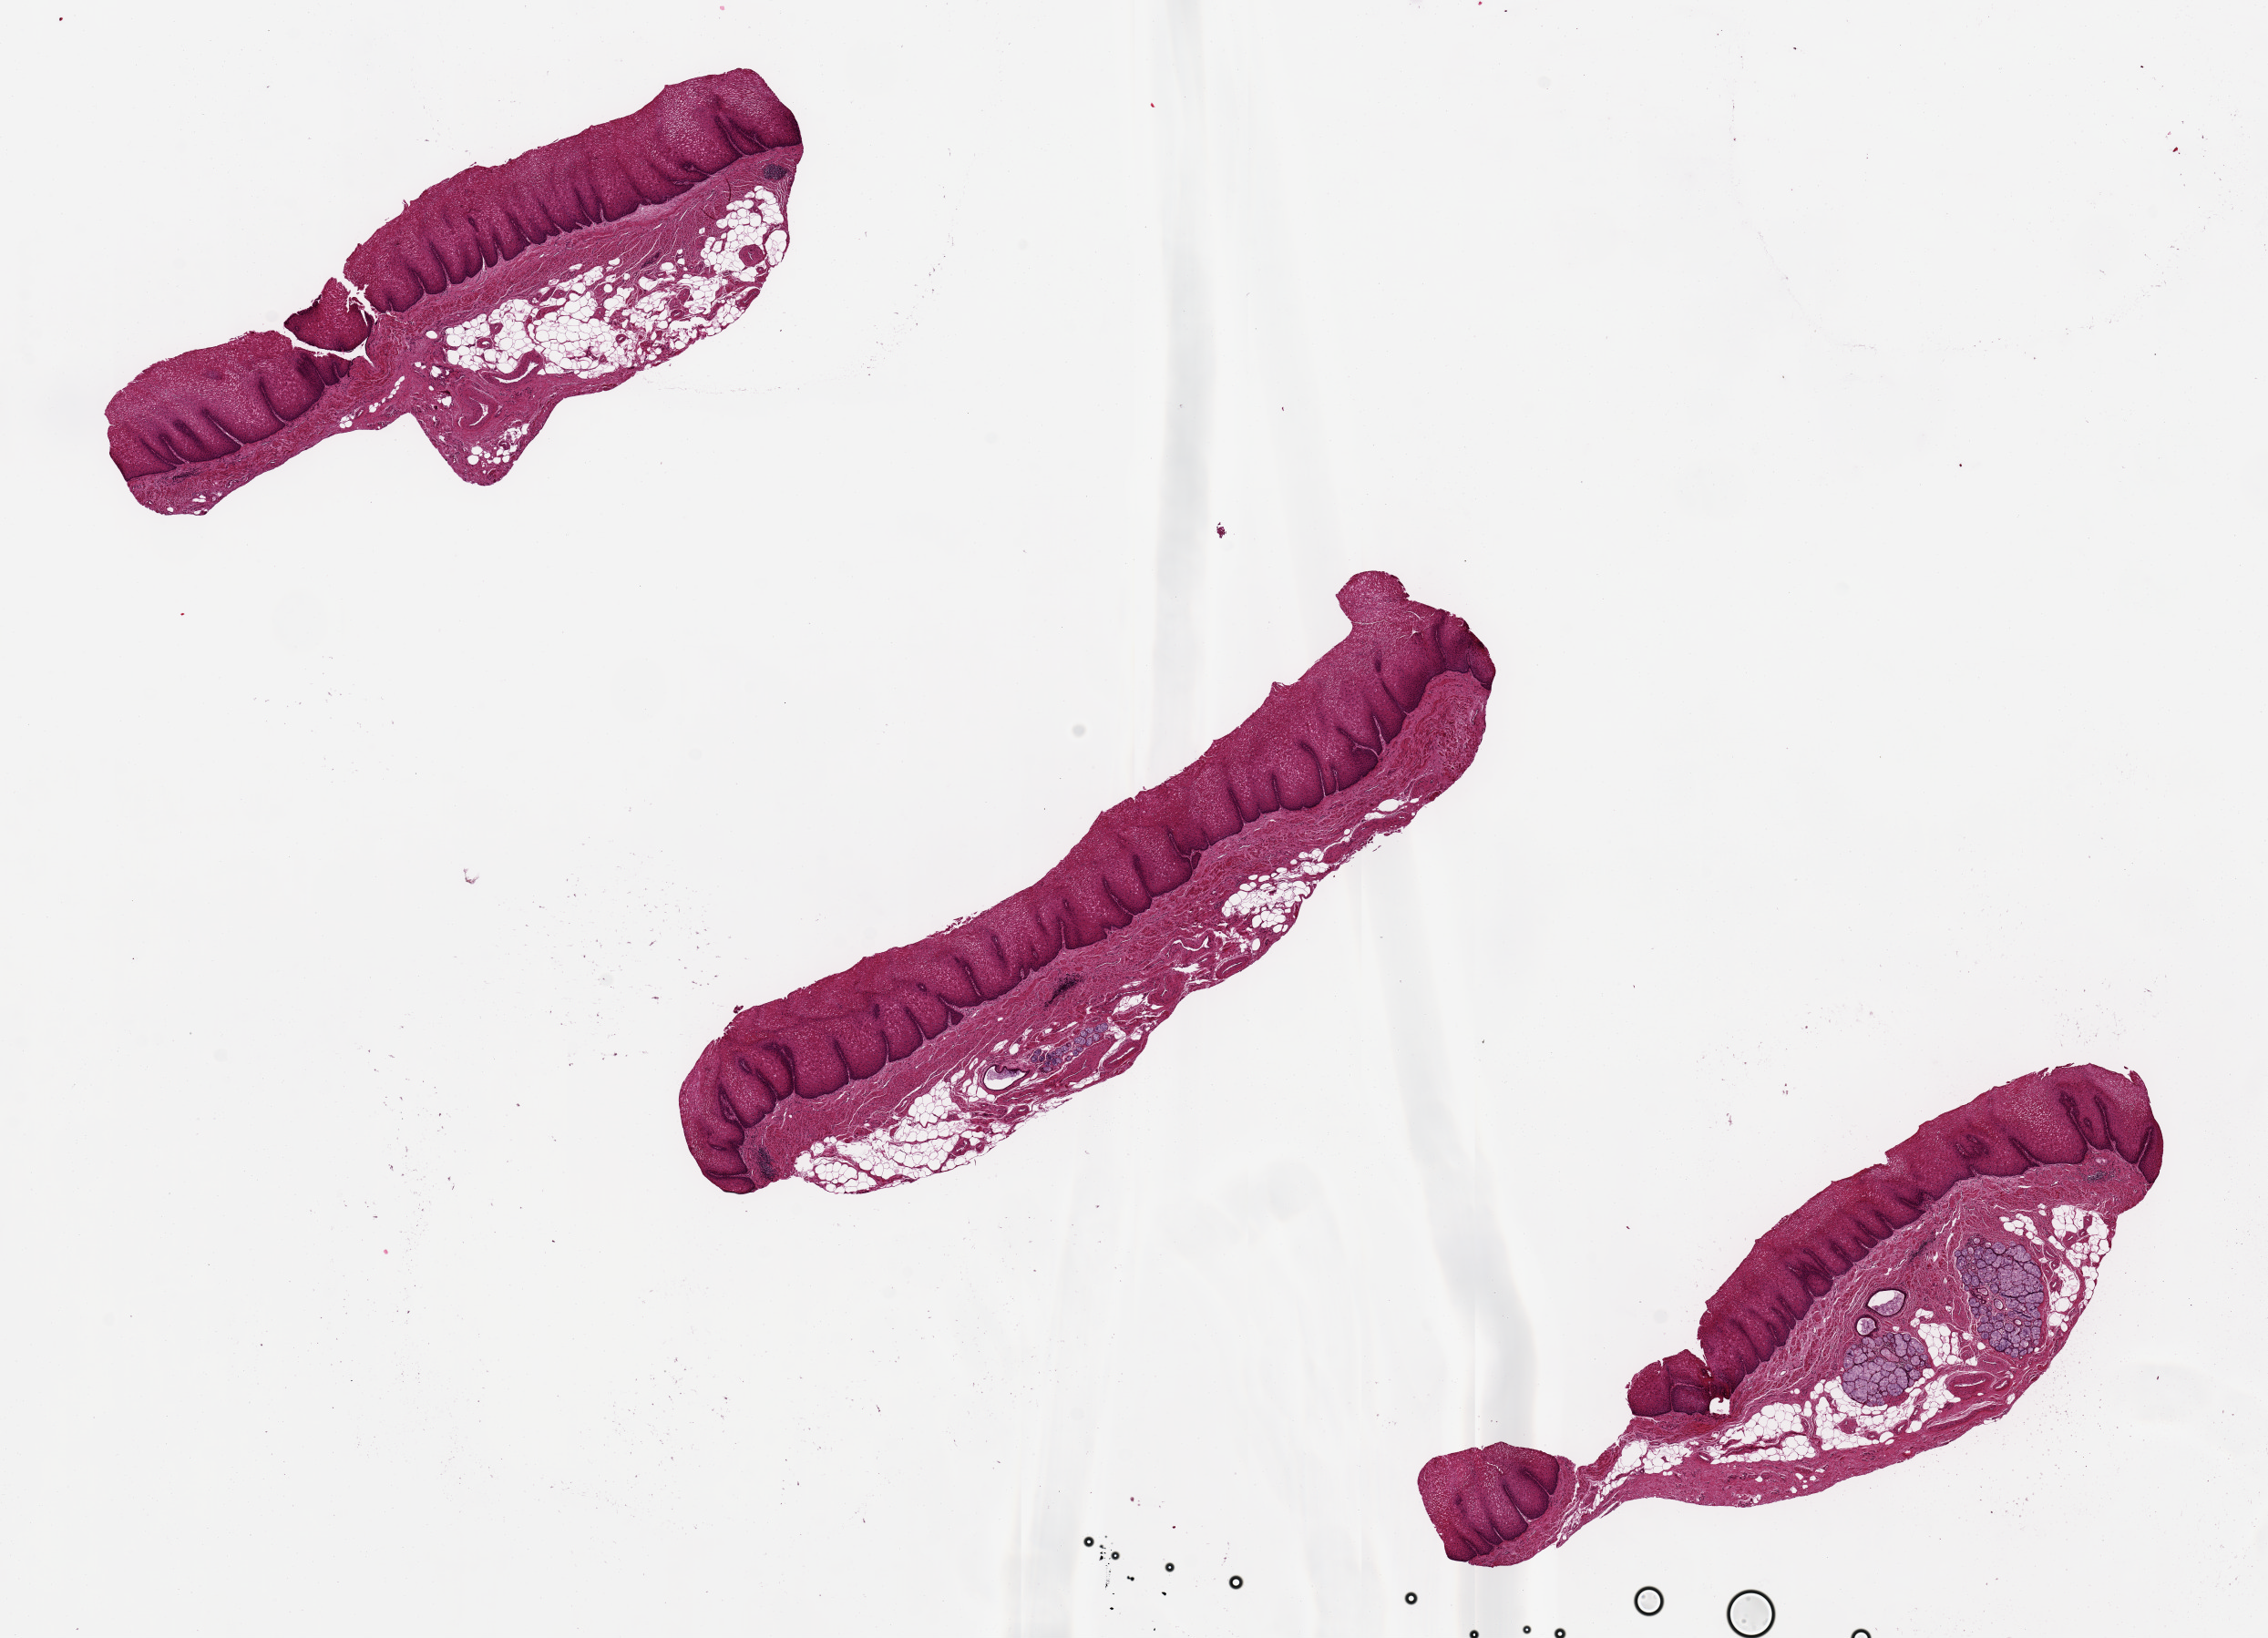
Digitized haematoxylin and eosin-stained section, brightfield — a low-resolution overview of the entire scanned area, about 19.7 x 14.2 mm (slide scanned at 20x). PAXgene-fixed paraffin-embedded (PFPE) section. Sampled site (target tissue): esophageal mucous membrane. Donor tissue sample. Donor: male.
Pathologist's review note for this sample: 3 pieces up to 8x2 mm. Squamous hyperplasia. Large submucosal glands in one piece.